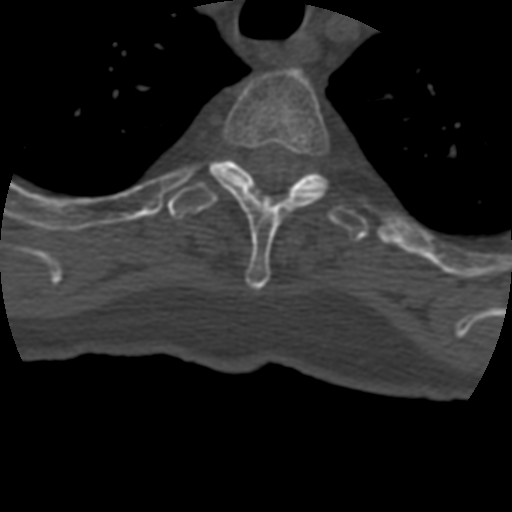
CT including the spine, one axial slice; slice 347 of 399 in the series (ordered by position); reconstruction kernel STANDARD; bone window (W 1800 / L 400 HU); 1.25 mm slice thickness; 512 × 512 image matrix, field of view 160 × 160 mm. Patient age 69 years. Case-level facts recorded for this patient, not image findings: primary cancer: prostate.
Annotated regions visible in this slice (semi-automatic segmentation, software-assisted and operator-edited):
- T3 vertebra: bounding box <210,69,329,290> (left, top, right, bottom; pixels)
- T4 vertebra: <167,159,370,242>